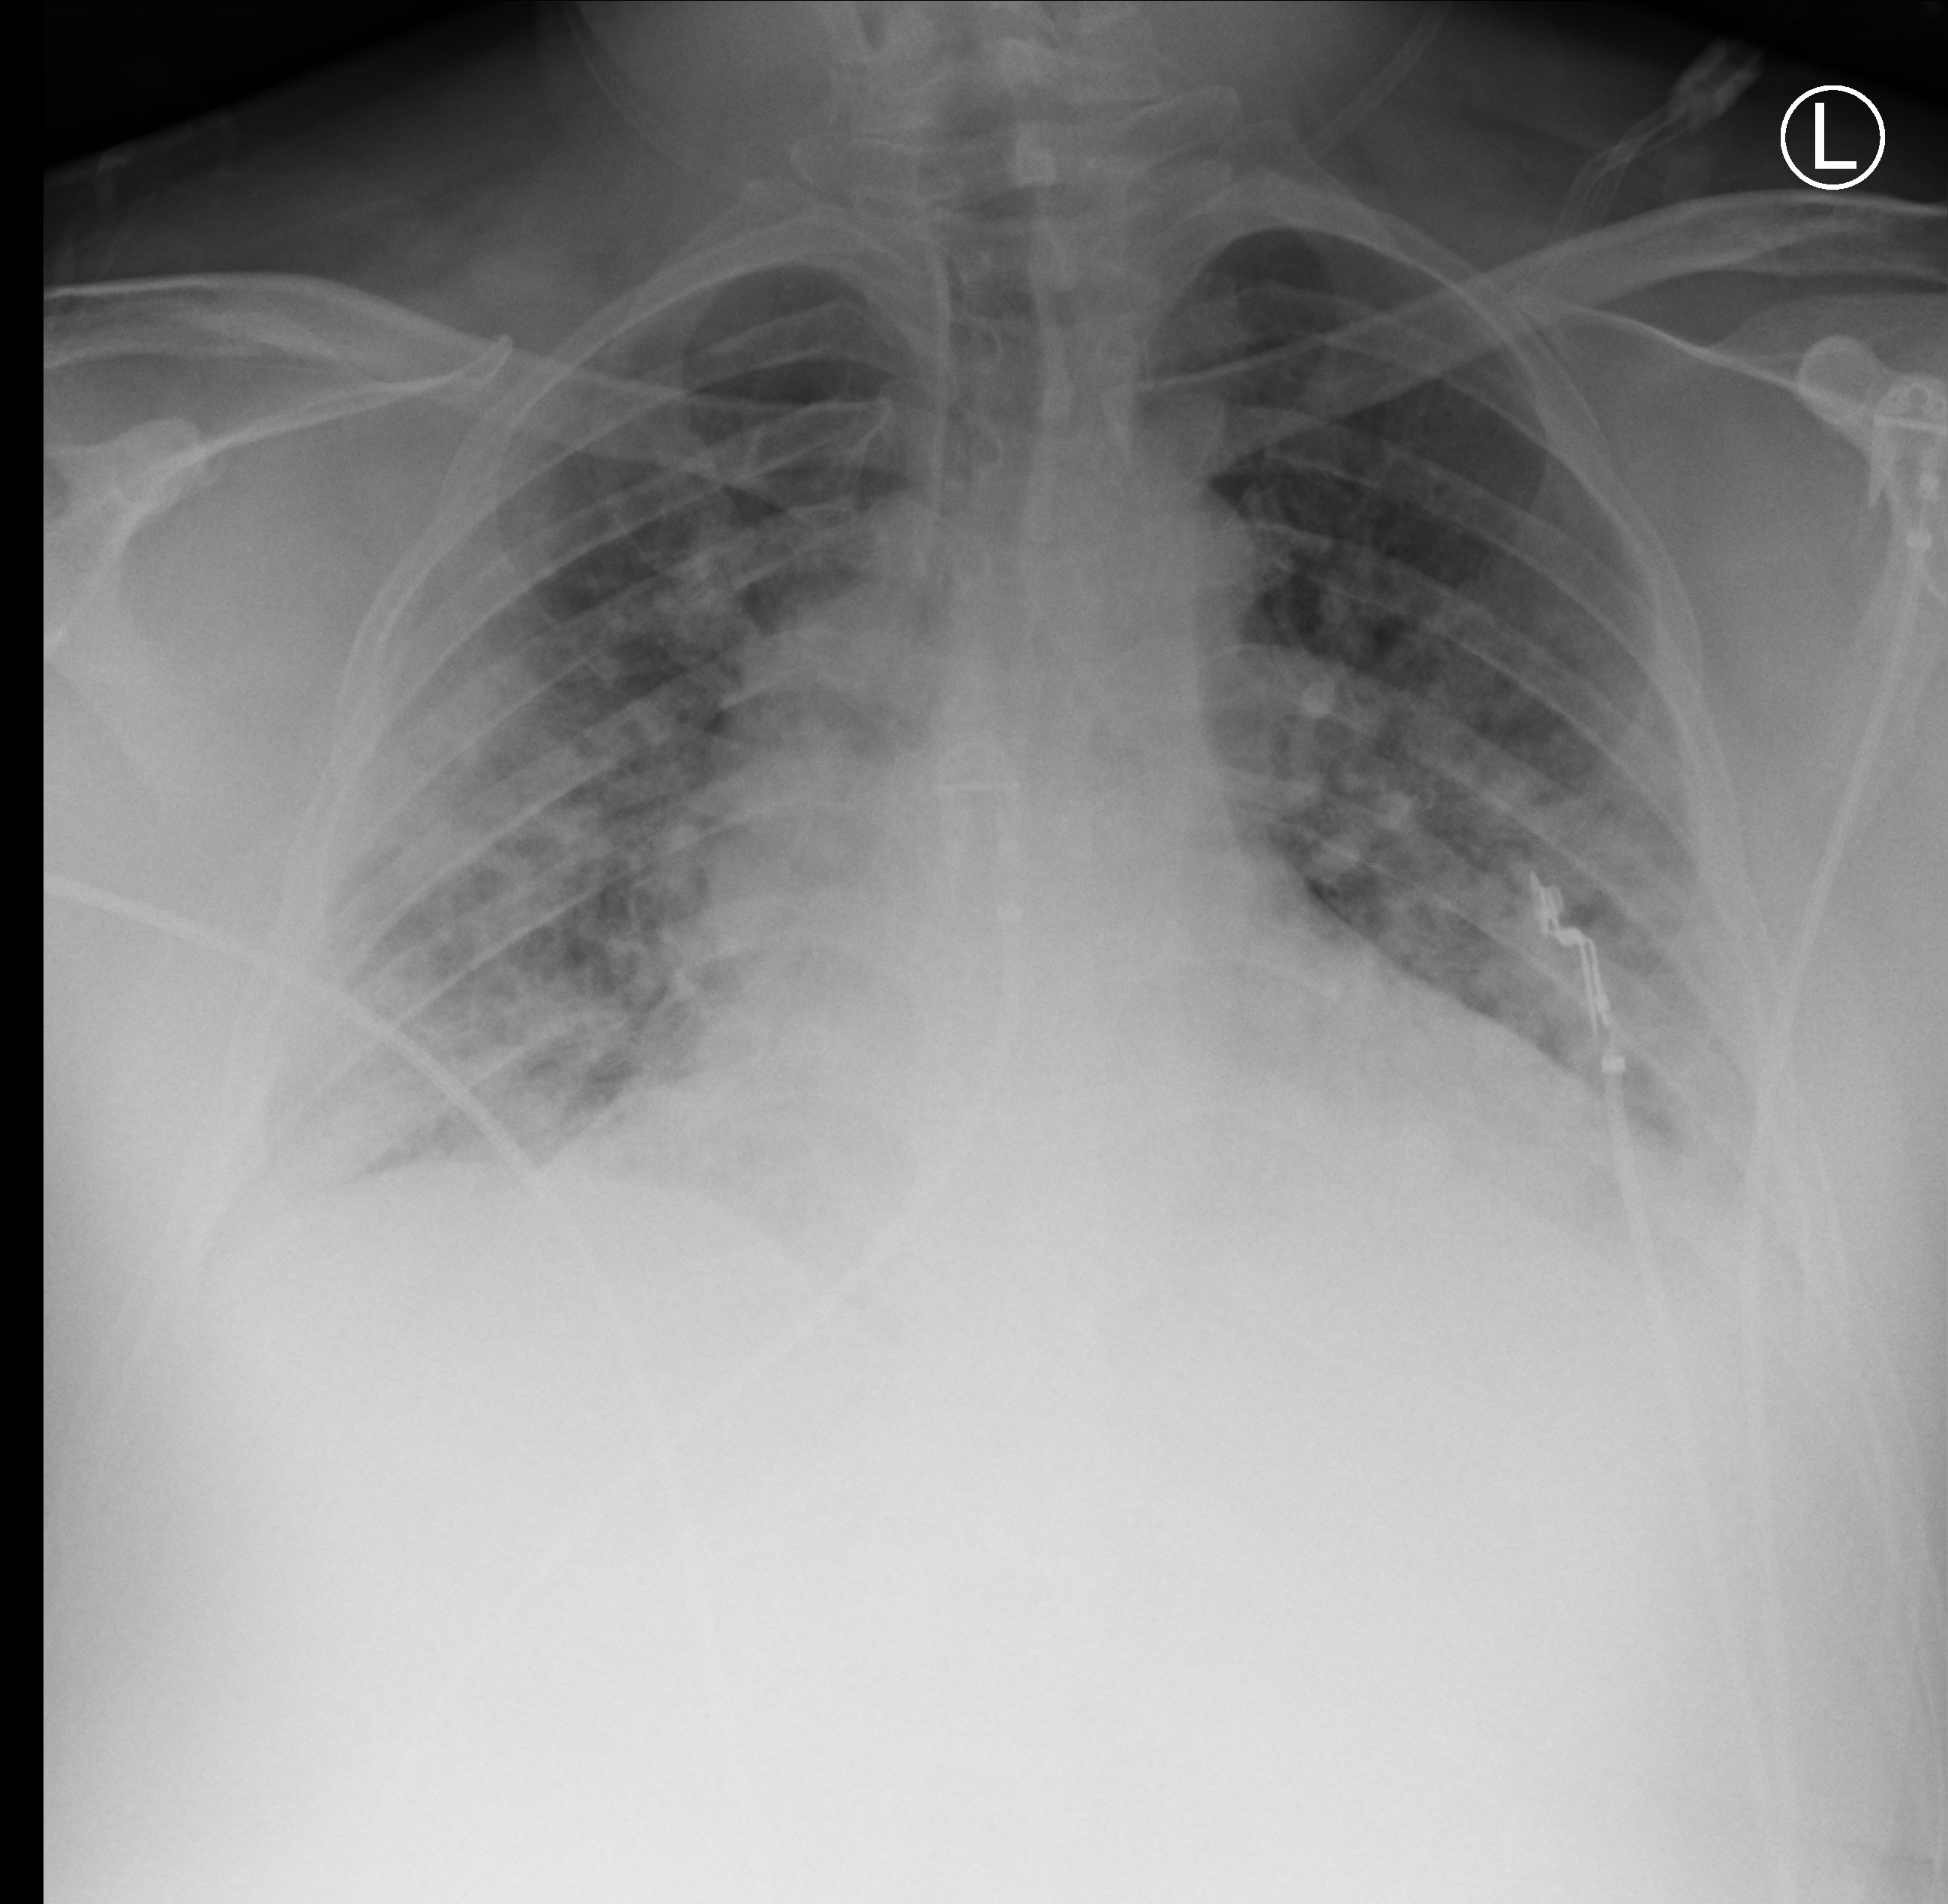
Chest X-ray (portable); anteroposterior (AP) projection. Patient hospitalised with COVID-19; male, aged 18–59 years.
Admission-level facts for this patient (not findings on this image; timing relative to this image not recorded): admitted to intensive care during this hospital stay: yes; mechanically ventilated during this hospital stay: yes.